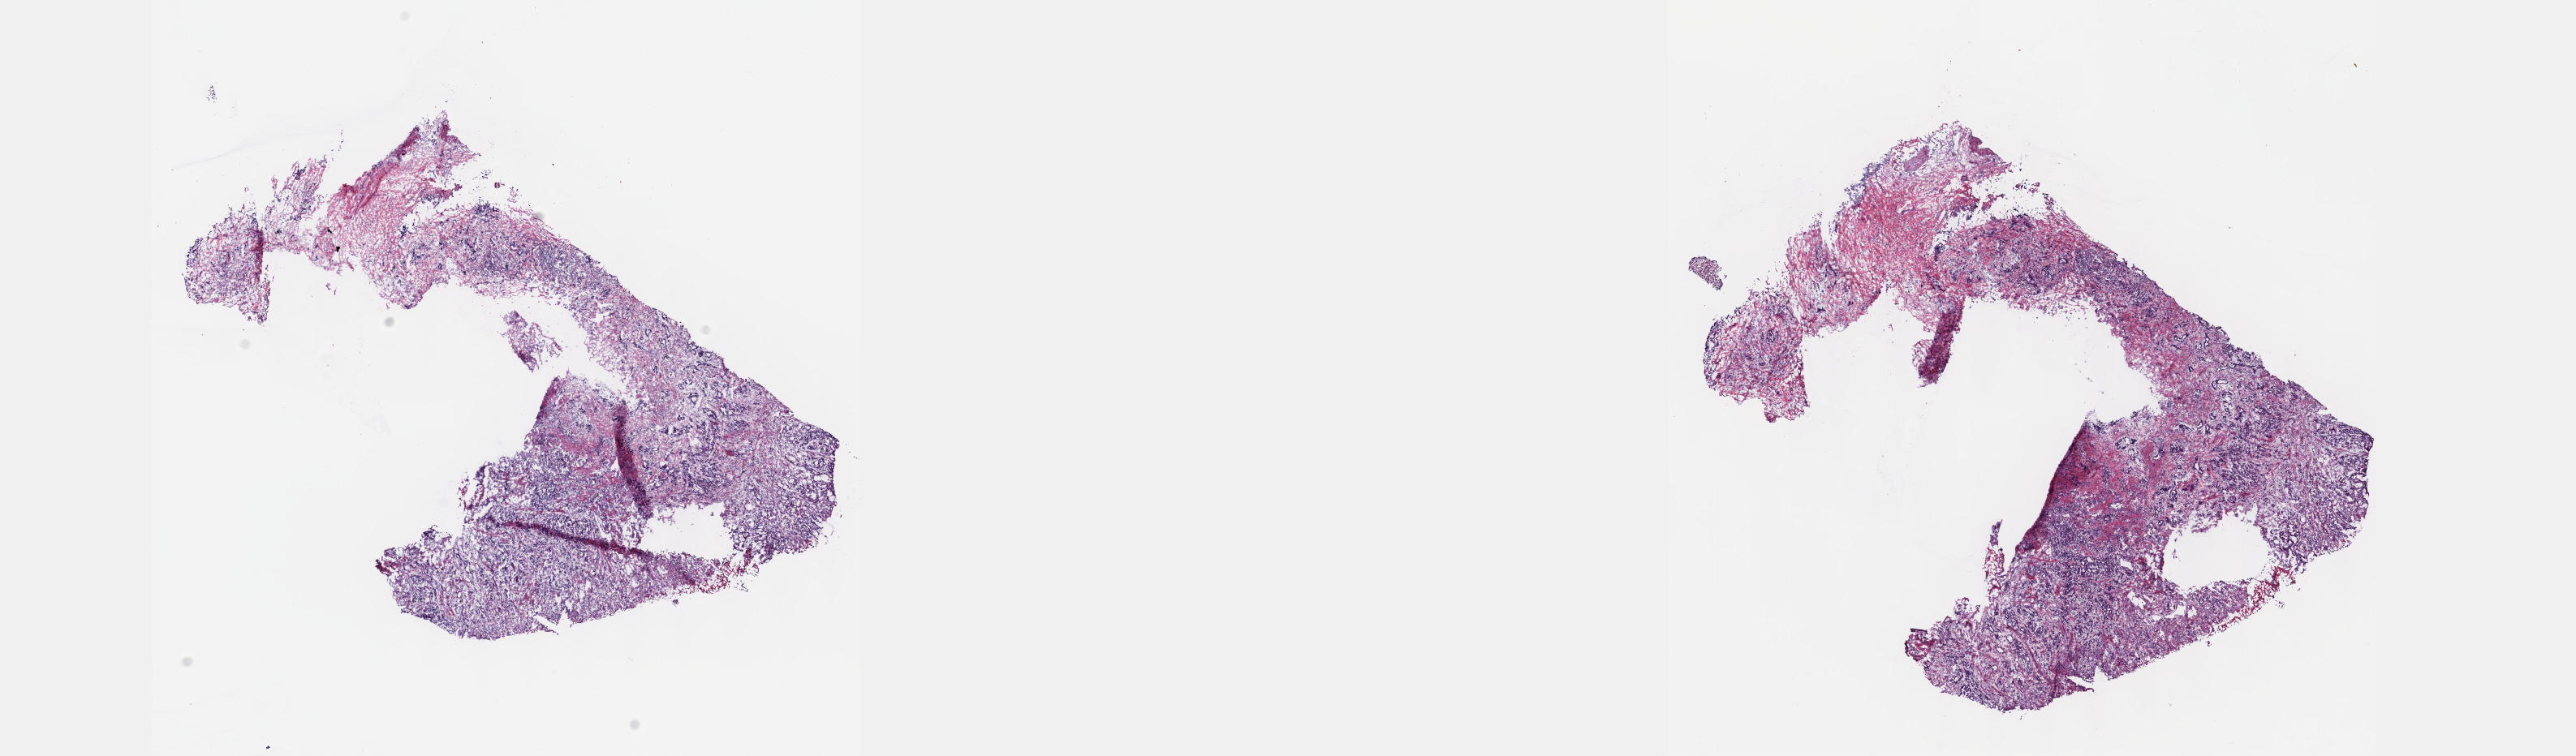
Digitized H&E tissue section (whole slide) — low-resolution overview of the scanned area, about 25.7 x 7.5 mm (acquisition: 40x scan); frozen section; sample: primary tumour, stomach. Male patient; age at initial diagnosis 63 years. Histologic grade: G2 (moderately differentiated). Composition of this section per pathologist review: tumour cells 32%, tumour nuclei 85%, normal cells 0%, stromal cells 65%, necrosis 3%. Infiltration values recorded for this section: lymphocyte infiltration 10%, monocyte infiltration 2%, neutrophil infiltration 1%.
Histologic diagnosis: Adenocarcinoma, intestinal type (gastric antrum).